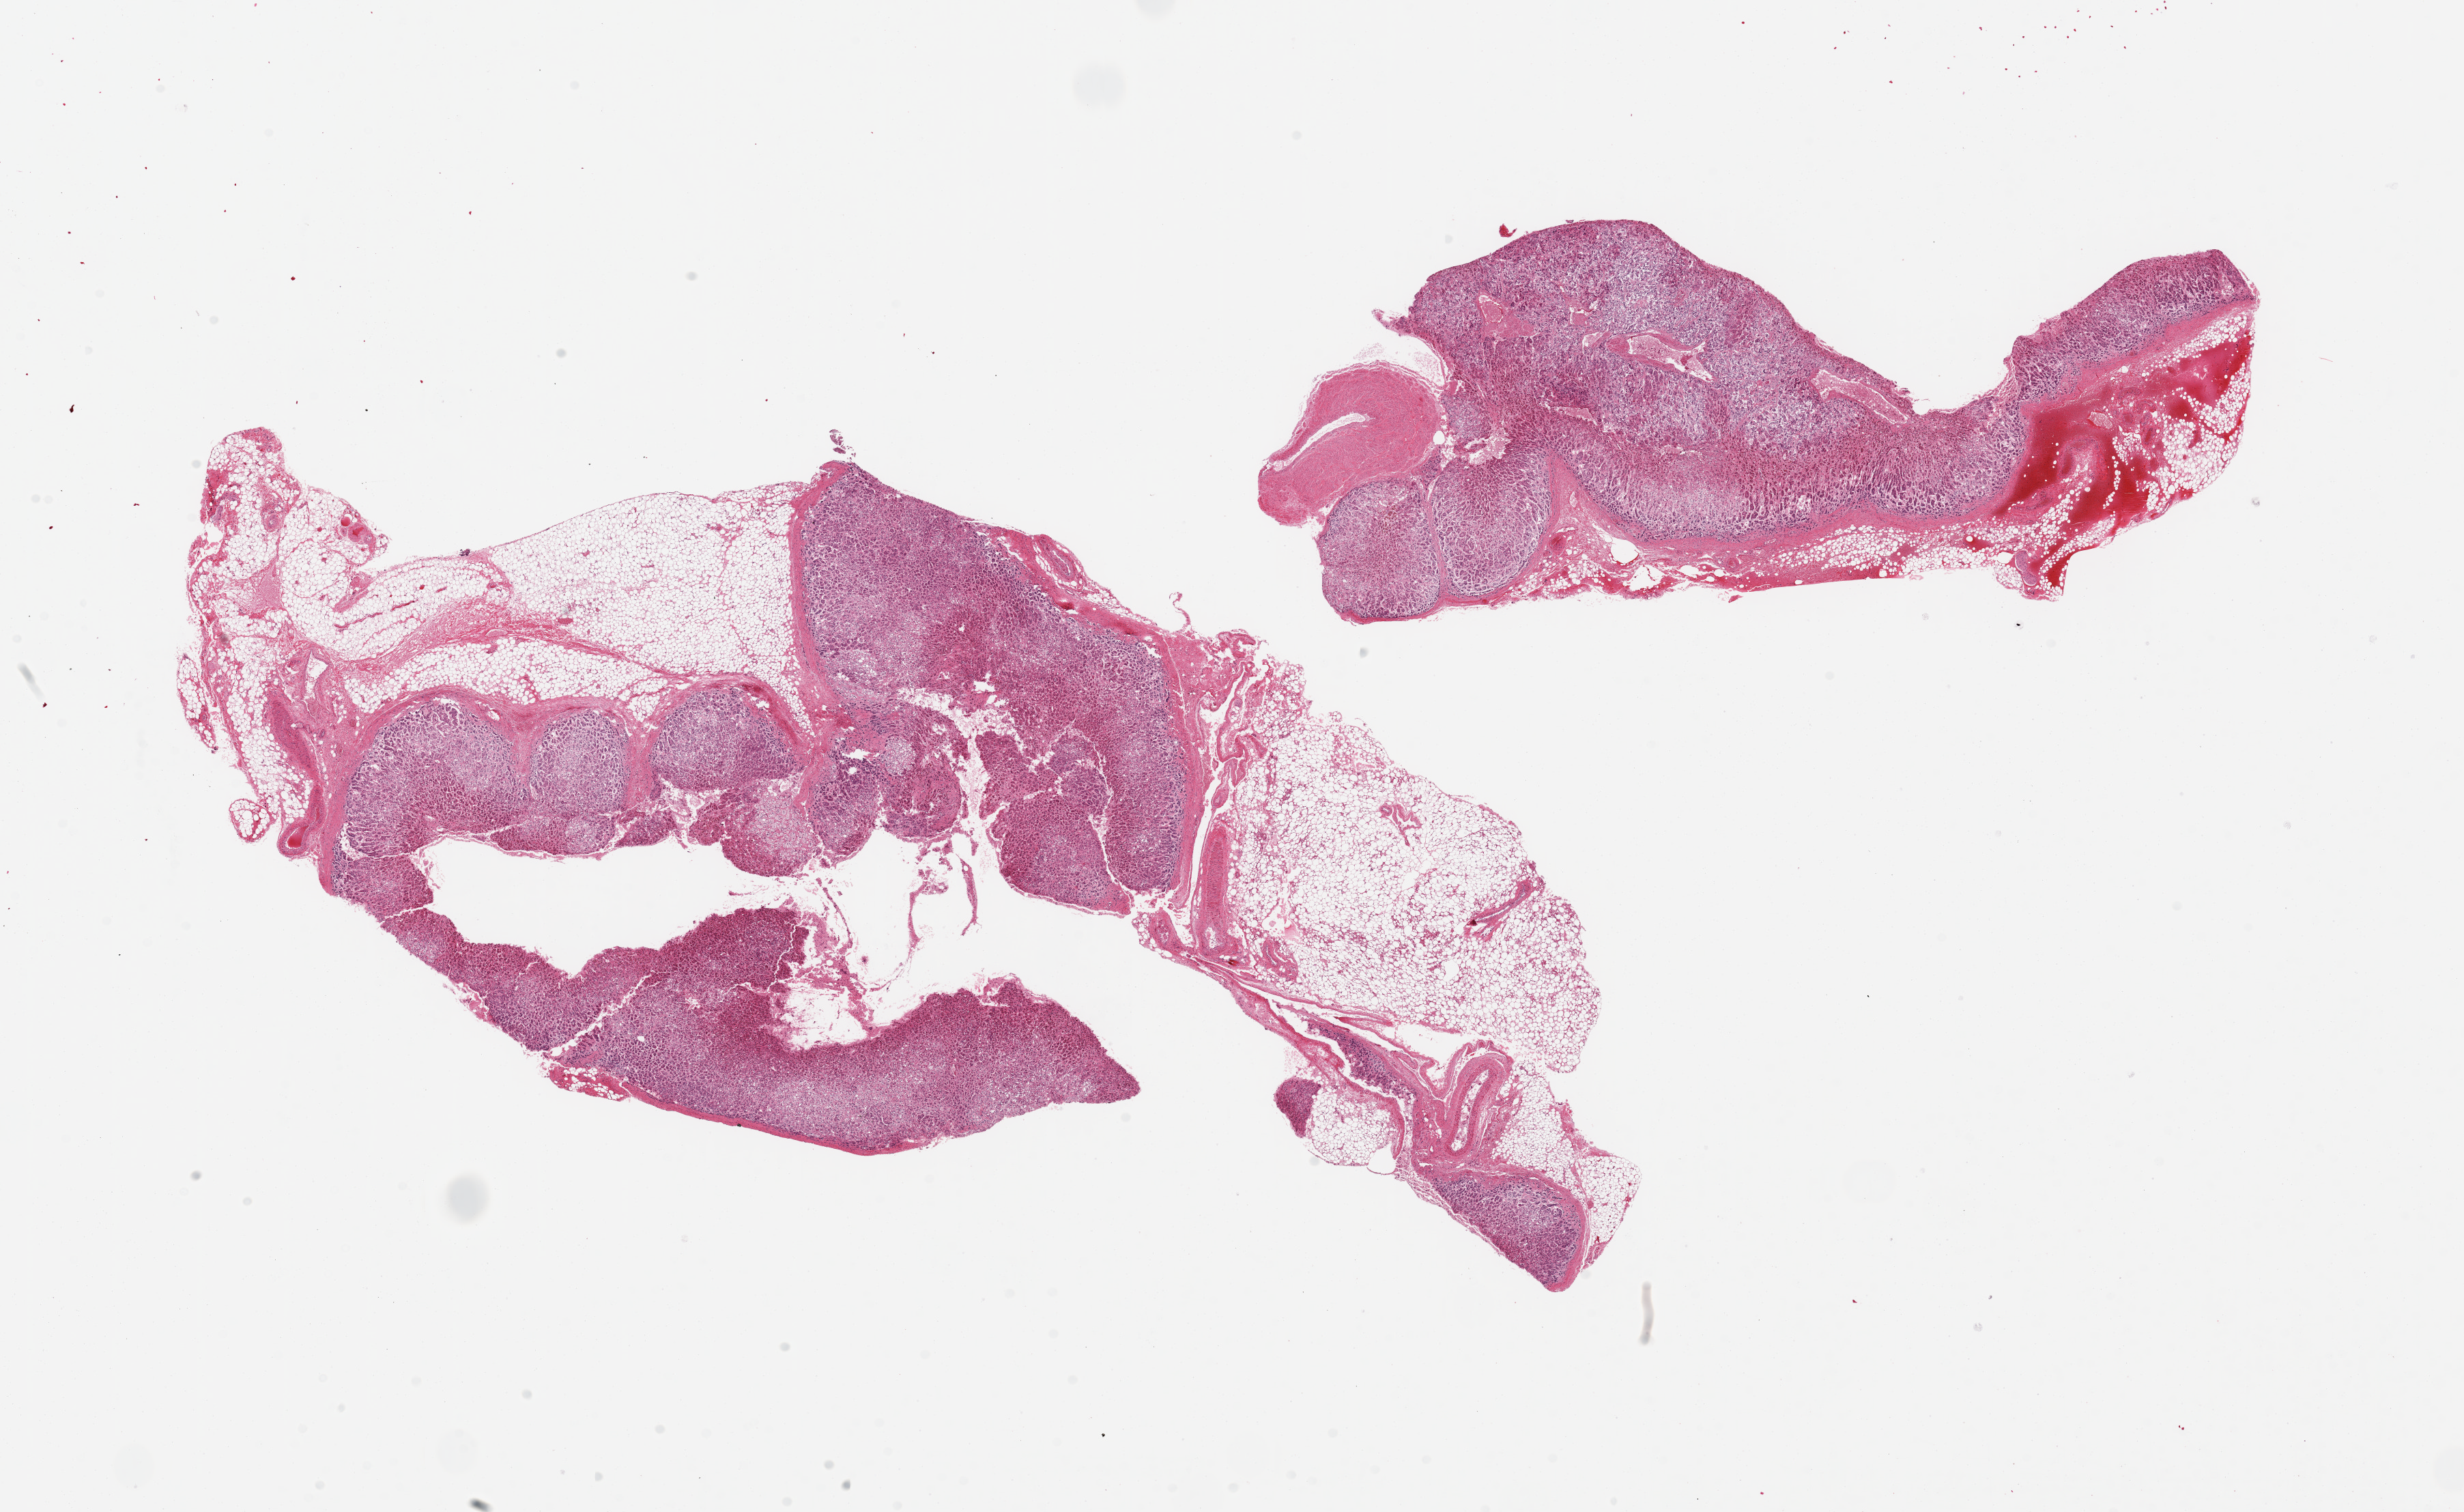
H&E whole-slide image, brightfield — shown as a low-resolution overview of the whole scanned area (about 28.5 x 17.5 mm, slide scanned at 20x). PAXgene-fixed paraffin-embedded (PFPE) section. Section of adrenal gland (target tissue). Tissue donor sample.
Review note (as recorded): 2 pieces, 18x8 & 11x4 mm; ~40% adipose; large, 2 mm, vein at periphery of 1 piece.